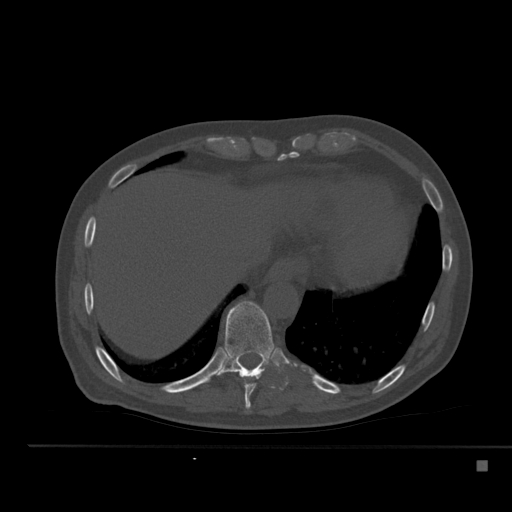
CT including the spine, one axial slice; slice 274 of 517 in the series (ordered by position); reconstruction kernel Br40s; bone window (W 1800 / L 400 HU); 512 × 512 image matrix, field of view 408 × 408 mm. Male patient, age 70 years. Case-level facts recorded for this patient, not image findings: primary cancer: renal; vertebrae with lytic lesions (as recorded): T4, T6, T10, T12, L3, L4, L5.
Annotated regions visible in this slice (semi-automatic segmentation, software-assisted and operator-edited):
- T10 vertebra: bounding box [x1, y1, x2, y2] px = [220, 301, 275, 378]
- T9 vertebra: [244, 376, 258, 410]